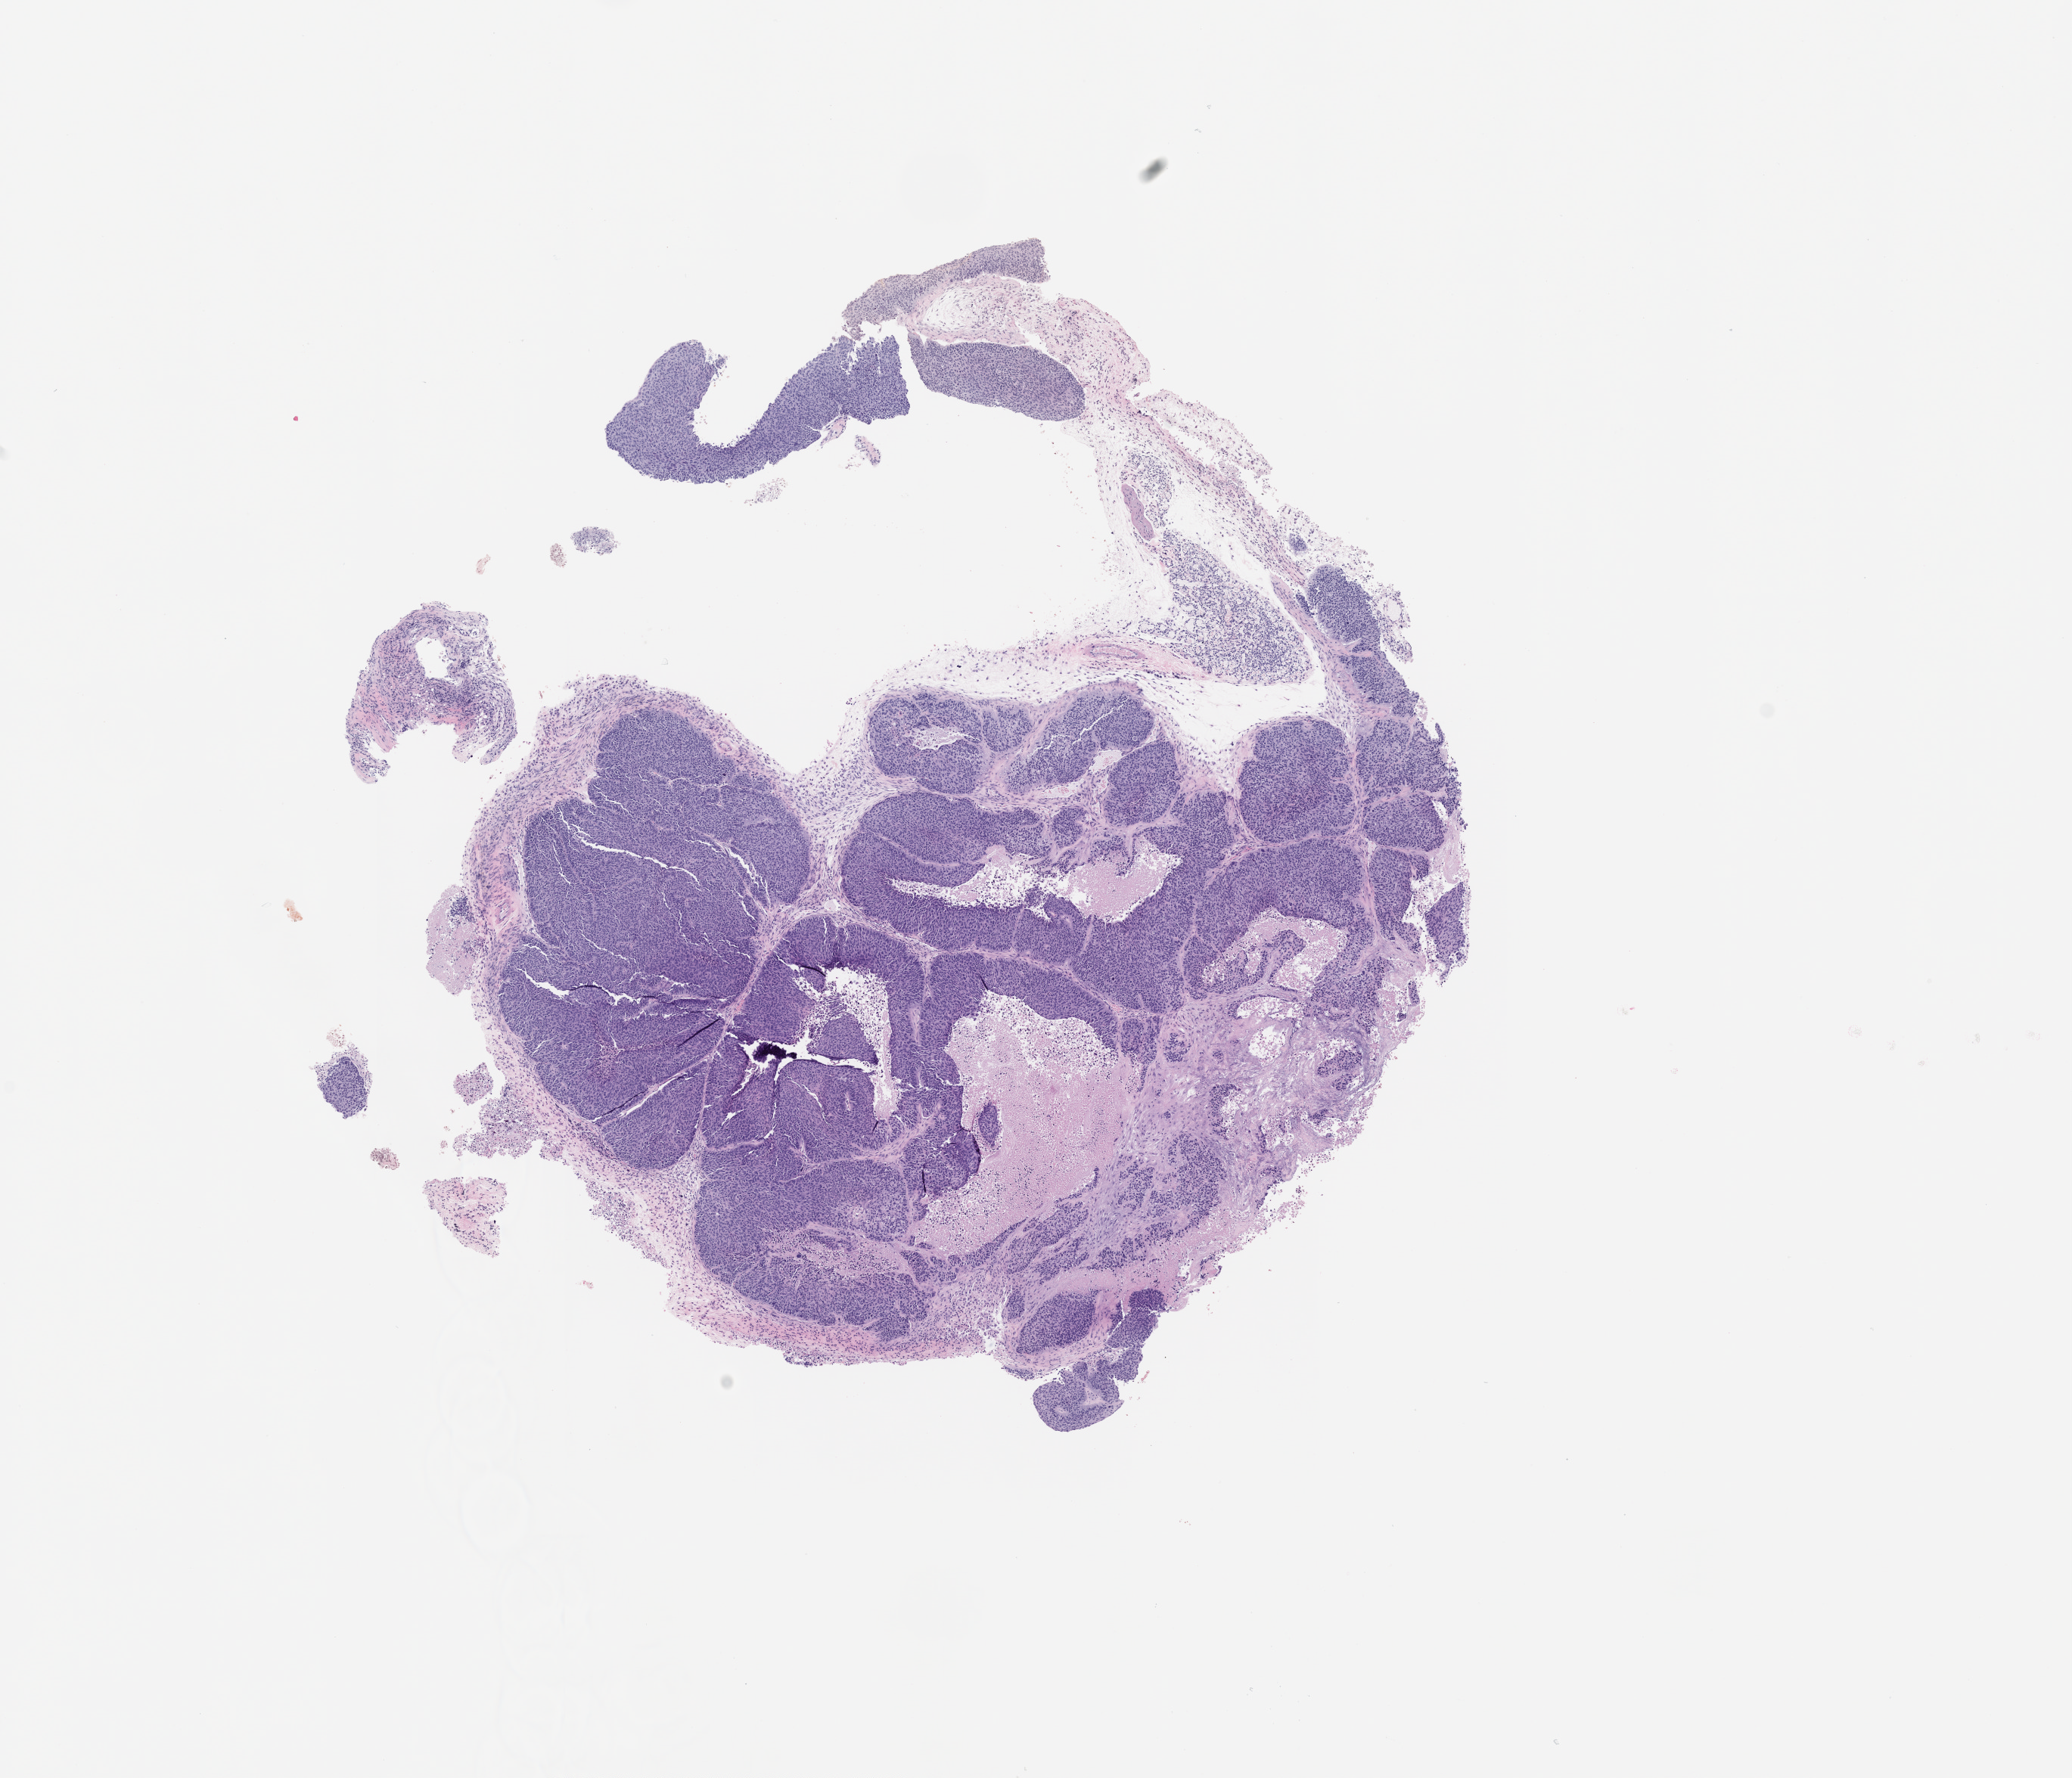
H&E whole-slide image of a patient-derived xenograft (PDX) tumor grown in a mouse, passage 2 — whole scanned area (about 11.0 x 9.5 mm) shown as a low-resolution overview, formalin-fixed, paraffin-embedded (FFPE) tissue, tumor site category: lung.
- originating patient diagnosis: Lung Squamous Cell Carcinoma